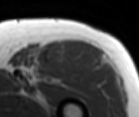
MRI of an extremity soft-tissue mass, one axial slice. Slice 72 of 86 in the series (ordered by position). MR volume resampled by the dataset authors to the PET/CT grid (not the native acquisition matrix). 3.27 mm slice thickness. 139 × 117 image matrix. Male patient. Case-level facts recorded for this patient, not image findings: histological type: extraskeletal osteosarcoma; grade: high; site of the primary tumour: thigh.
Structures marked on this image (expert contour drawn on MRI and transferred to this co-registered scan by the dataset authors):
- gross tumour volume (mass): box from (x=47, y=41) to (x=103, y=72) px